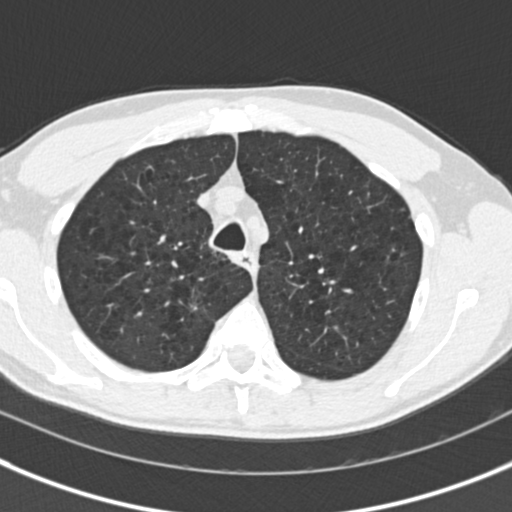
Low-dose screening chest CT, one axial slice; slice 134 of 175 in the series (ordered by position); reconstruction kernel B30f; lung window (W 1500 / L -600 HU); 2 mm slice thickness; 512 × 512 image matrix, field of view 306 × 306 mm.
Structures marked on this image (manually delineated by an expert):
- lesion 2 (tumor, upper lobe of right lung): box from (x=191, y=306) to (x=197, y=310) px